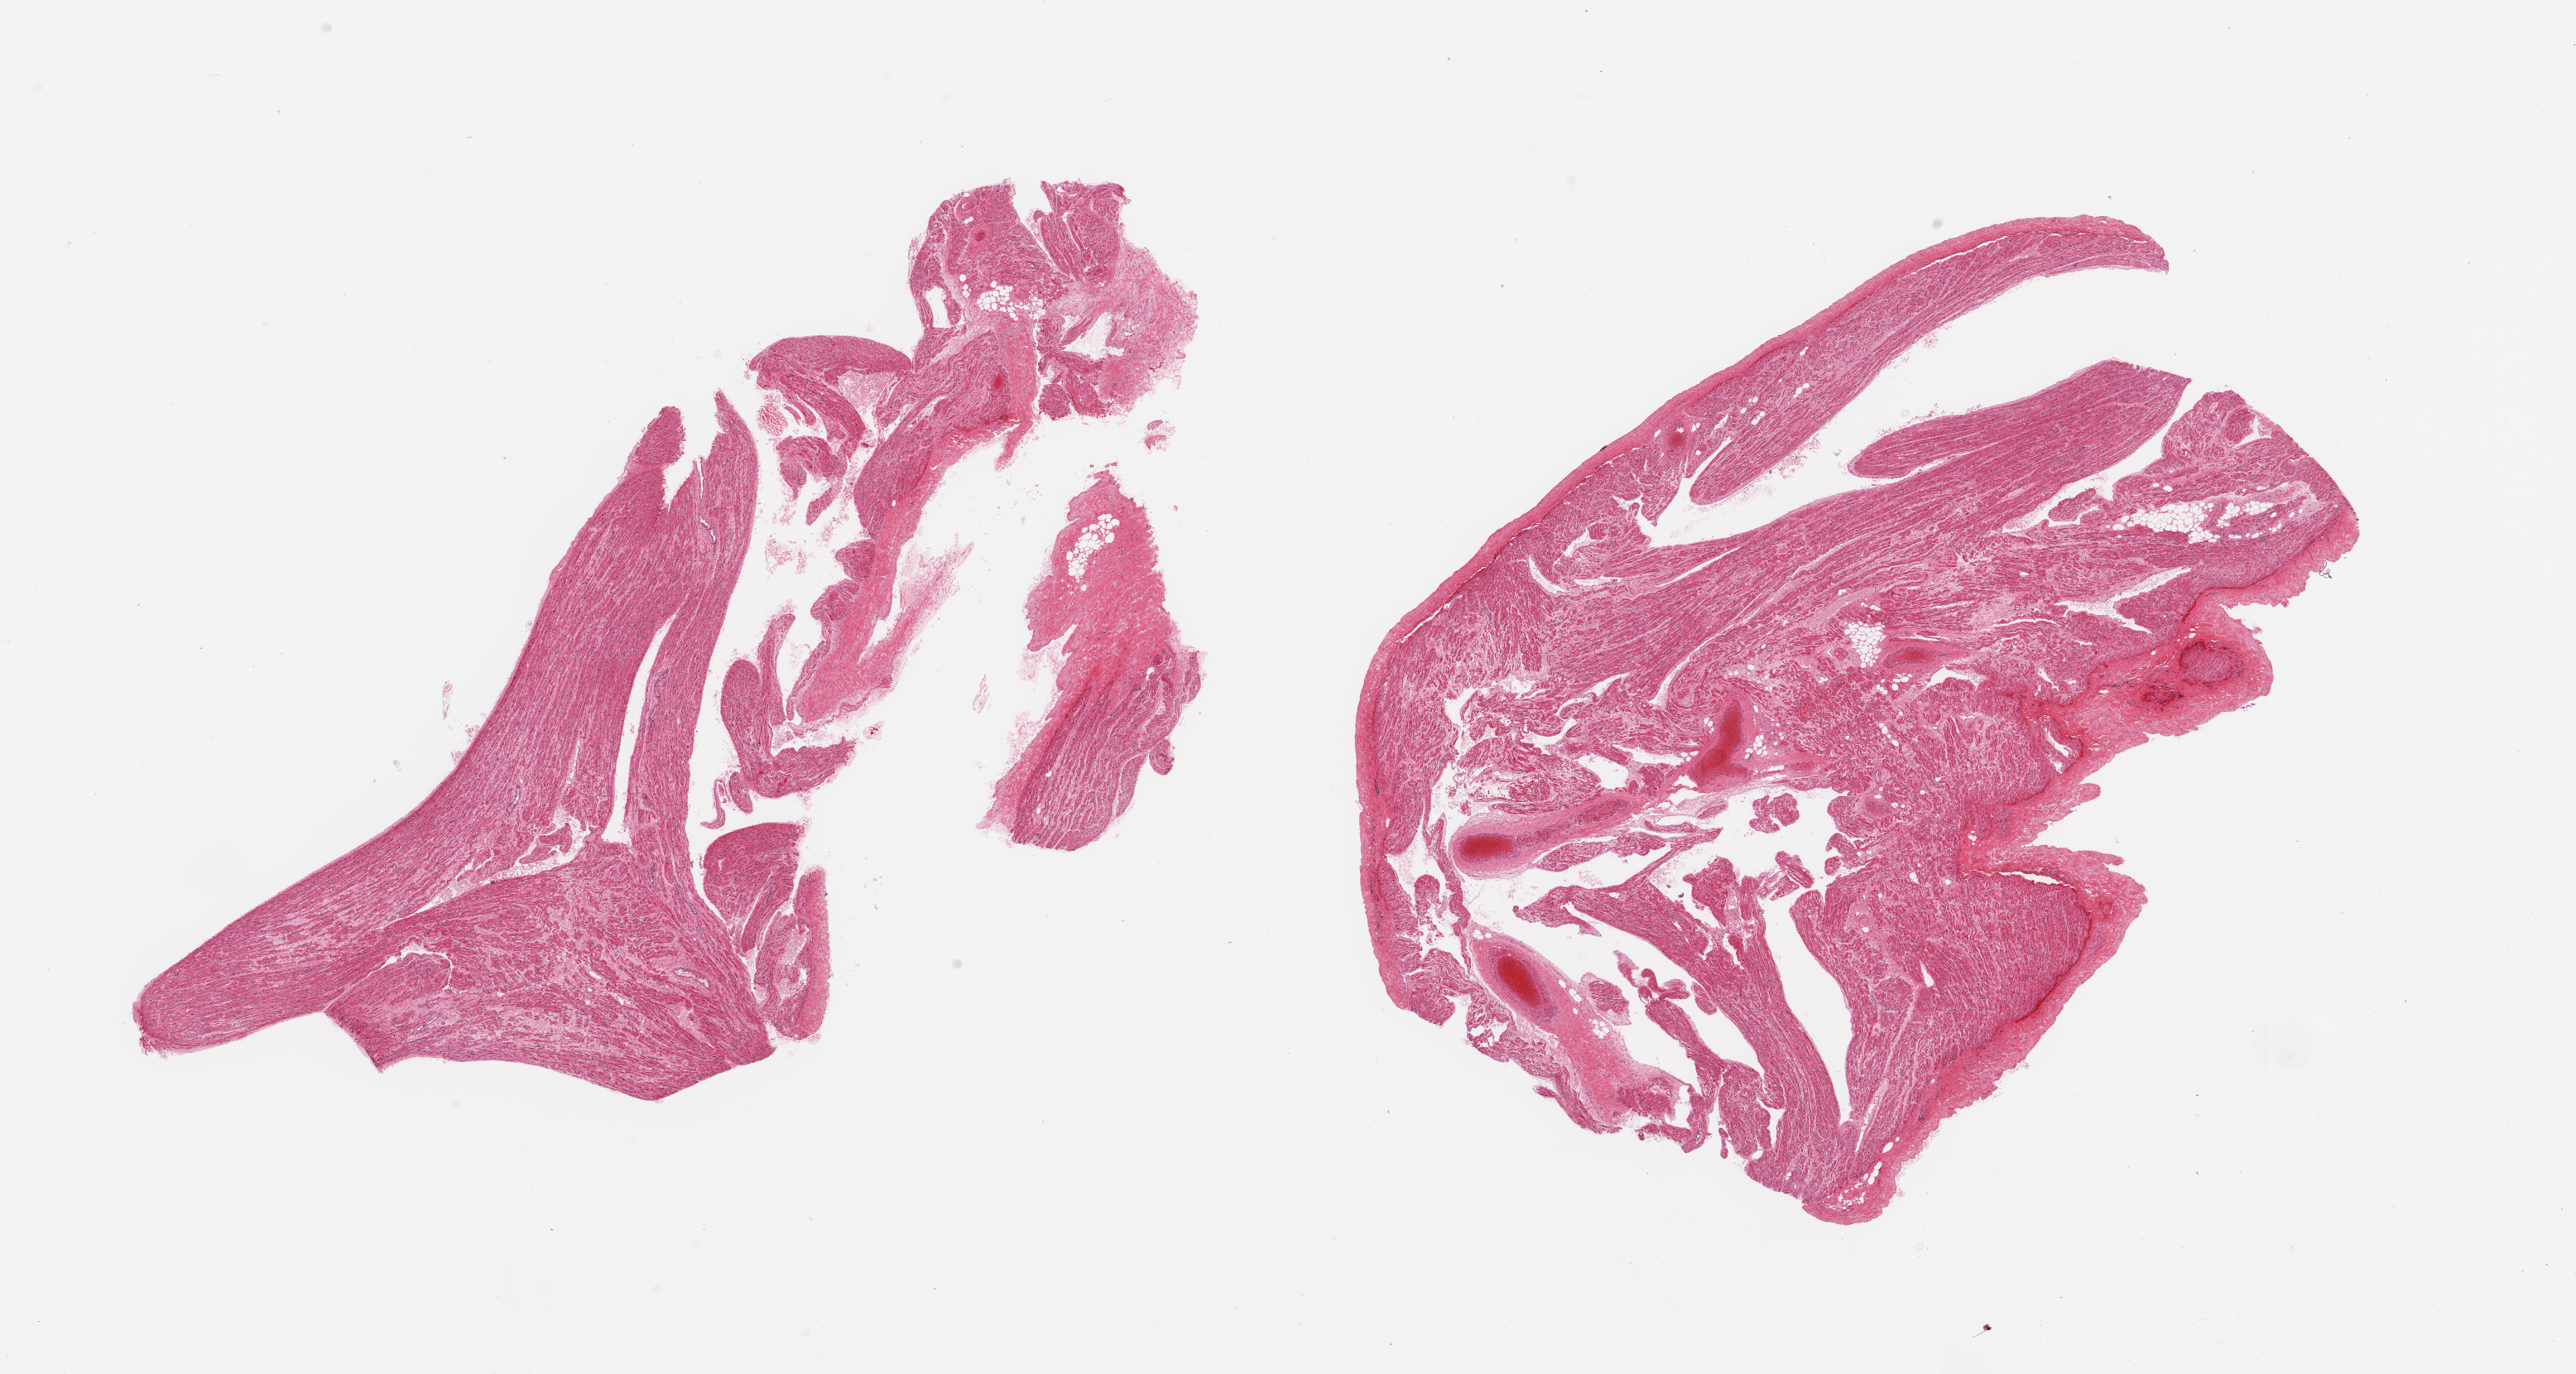
Whole-slide image, hematoxylin and eosin (H&E) stain, whole scanned area (about 24.6 x 13.1 mm) shown as a low-resolution overview, PAXgene-fixed, paraffin-embedded tissue, target tissue: auricular appendage, tissue donor sample. Male donor.
Pathologist's review note for this sample: 2 pieces, no abnormalities.